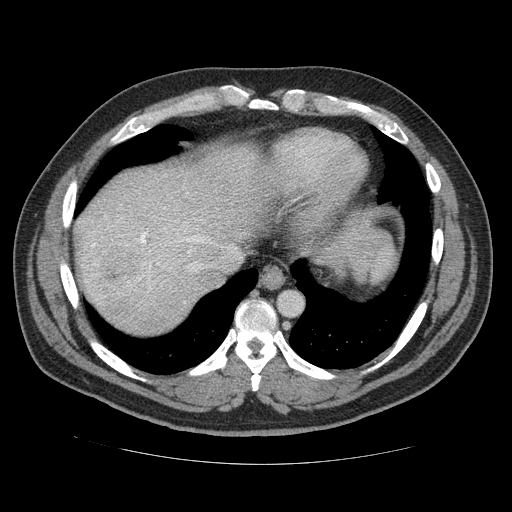
Contrast-enhanced abdominal CT (liver protocol), one axial slice; slice 103 of 113 in the series (ordered by position); reconstruction kernel STANDARD; 120 kVp; soft-tissue window (W 400 / L 40 HU); 512 × 512 image matrix. Case-level facts recorded for this patient, not image findings: diagnosis: hepatocellular carcinoma (patient treated with transarterial chemoembolisation; whether this scan precedes or follows treatment is not stated here); TNM stage (as recorded): Stage-II; Child-Pugh class: B; tumour differentiation: moderately differentiated; tumour nodularity: multinodular.
Outlined on this slice (semi-automatically segmented with operator editing):
- abdominal aorta: bounding box <279,292,302,315> (left, top, right, bottom; pixels)
- liver parenchyma outside the tumour (the mass and vessels are separate outlines, so this box may not span the whole liver): <76,152,258,330>
- mass: <91,240,148,293>
- liver vessels: <90,228,152,270>